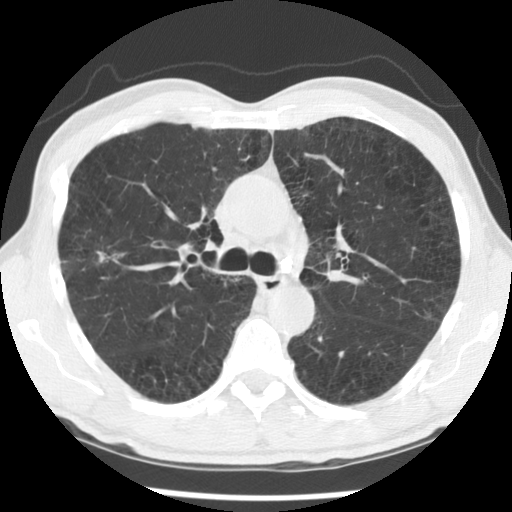
Low-dose screening chest CT, axial slice; second annual screen; lung window (W 1500 / L -600 HU); 2.5 mm slice thickness; standard (soft-tissue) reconstruction kernel (STANDARD); slice 85 of 138 in the series; 512 × 512 image matrix. Male, age 56 years at enrolment. Current smoker at enrolment.
Expert reader's lesion annotation, bounding box [x1, y1, x2, y2] px = [50, 231, 137, 291]. The exam's reader record, not a measurement of the box and not confirmed to be the same lesion: non-calcified nodule or mass ≥4 mm, right upper lobe, 30 × 18 mm, spiculated (stellate) margins, mixed attenuation, pre-existing on the prior screen: yes; interval growth: yes. Official screen result: positive, other.